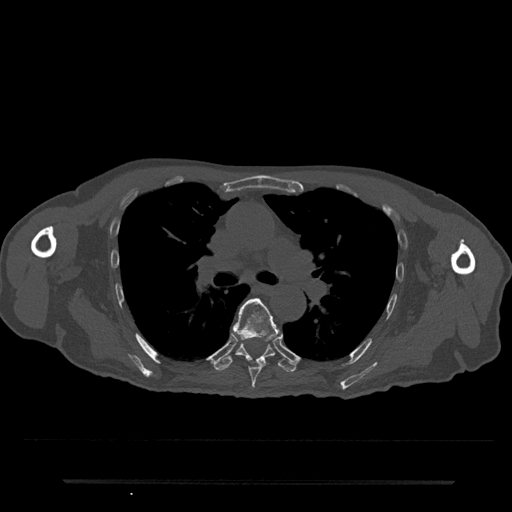
CT including the spine, one axial slice. Position 508 of 797 along the scan axis. 120 kVp. Bone window (W 1800 / L 400 HU). 0.5 mm slice thickness. 512 × 512 image matrix, field of view 427 × 427 mm. Patient: male, 74 years. Case-level facts recorded for this patient, not image findings: primary cancer: prostate.
Annotated regions visible in this slice (semi-automatic segmentation, software-assisted and operator-edited):
- T6 vertebra: box from (x=232, y=298) to (x=279, y=389) px
- T7 vertebra: (x=215, y=343)–(x=296, y=372)